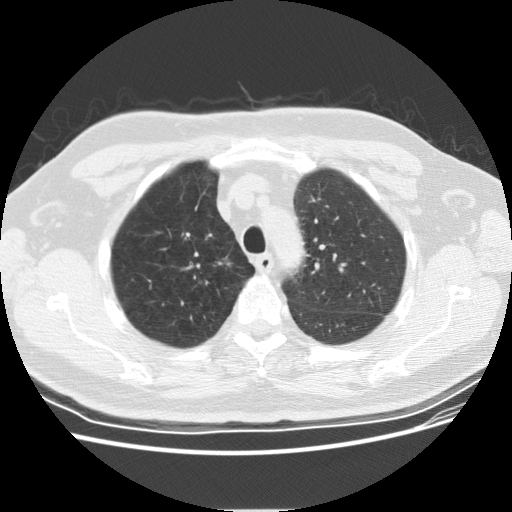
Chest CT (low-dose screening protocol), one axial image; second annual screen; lung window (W 1500 / L -600 HU); standard (soft-tissue) reconstruction kernel (STANDARD); slice 116 of 152 in the series; 512 × 512 image matrix, field of view 360 × 360 mm. Male, age 69 years at enrolment. Current smoker at enrolment.
• Lesion marked by an expert reader, box from (x=208, y=245) to (x=242, y=278) px.
• The exam's reader record, not a measurement of the box and not confirmed to be the same lesion: non-calcified nodule or mass ≥4 mm, right lower lobe, 4 × 4 mm, smooth margins, soft tissue attenuation, pre-existing on the prior screen: yes; interval growth: no.
• Later outcome: lung cancer diagnosed 435 days after this screen (after the third annual screen) — squamous cell carcinoma, NOS, right upper lobe, moderately differentiated (G2), stage IA (AJCC 6th edition), 9 mm at pathology.